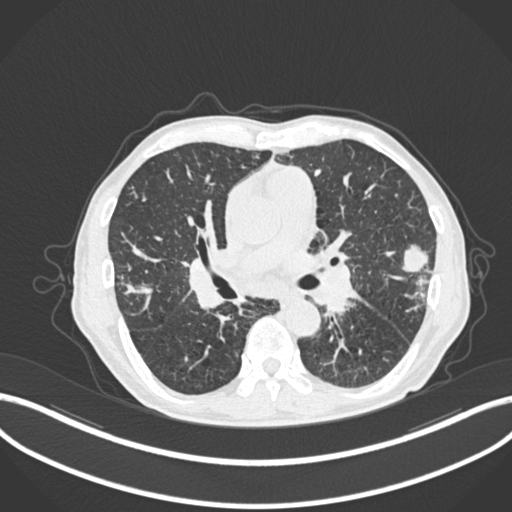
Chest CT, one axial slice. Position 124 of 287 along the scan axis. Reconstruction kernel B30f. 120 kVp. Lung window (W 1500 / L -600 HU). 512 × 512 image matrix, field of view 400 × 400 mm. Male patient, age 74 years. Case-level facts recorded for this patient, not image findings: clinical TNM (as recorded): T2a N1 M0.
Structures marked on this image (rectangle marked by the reading radiologist):
- lung tumour (recorded histology: adenocarcinoma): bounding box <398,243,430,279> (left, top, right, bottom; pixels)